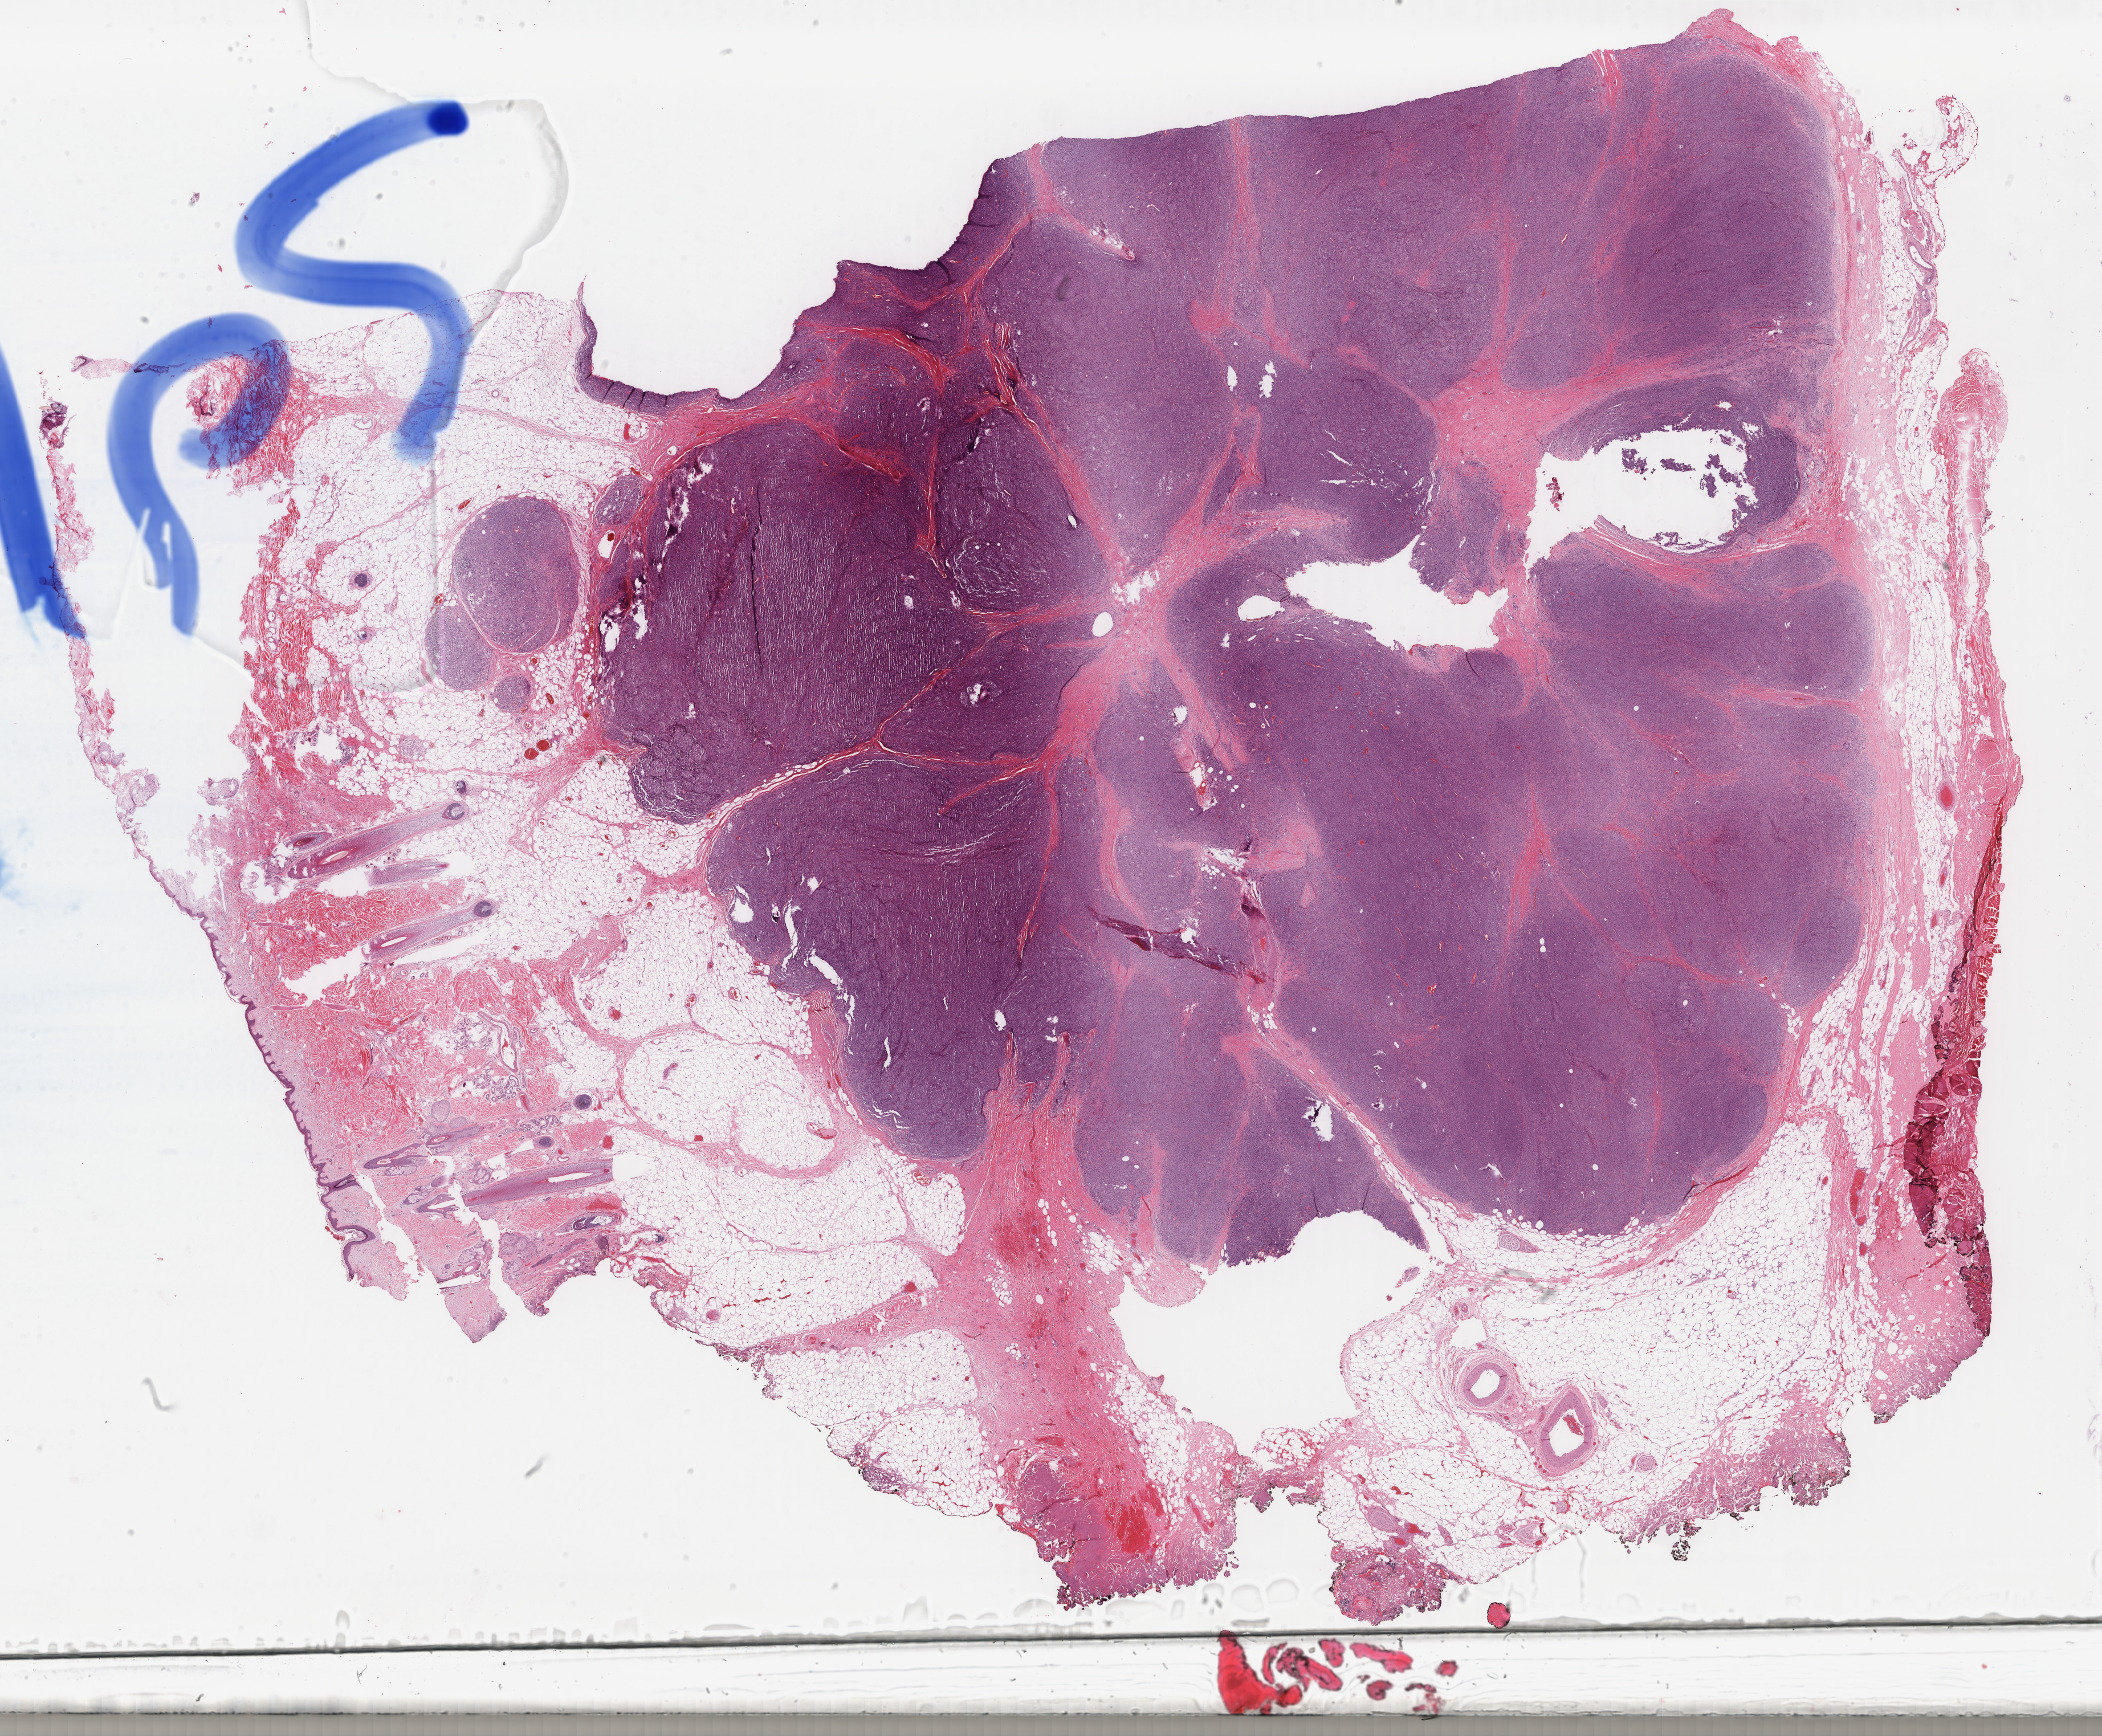
H&E-stained whole-slide image — low-resolution overview of the scanned area, about 29.3 x 24.2 mm, formalin-fixed paraffin-embedded (FFPE) diagnostic section, skin, primary tumour sample. Male patient; age at initial diagnosis 54 years.
Pathologic diagnosis: Malignant melanoma, NOS.